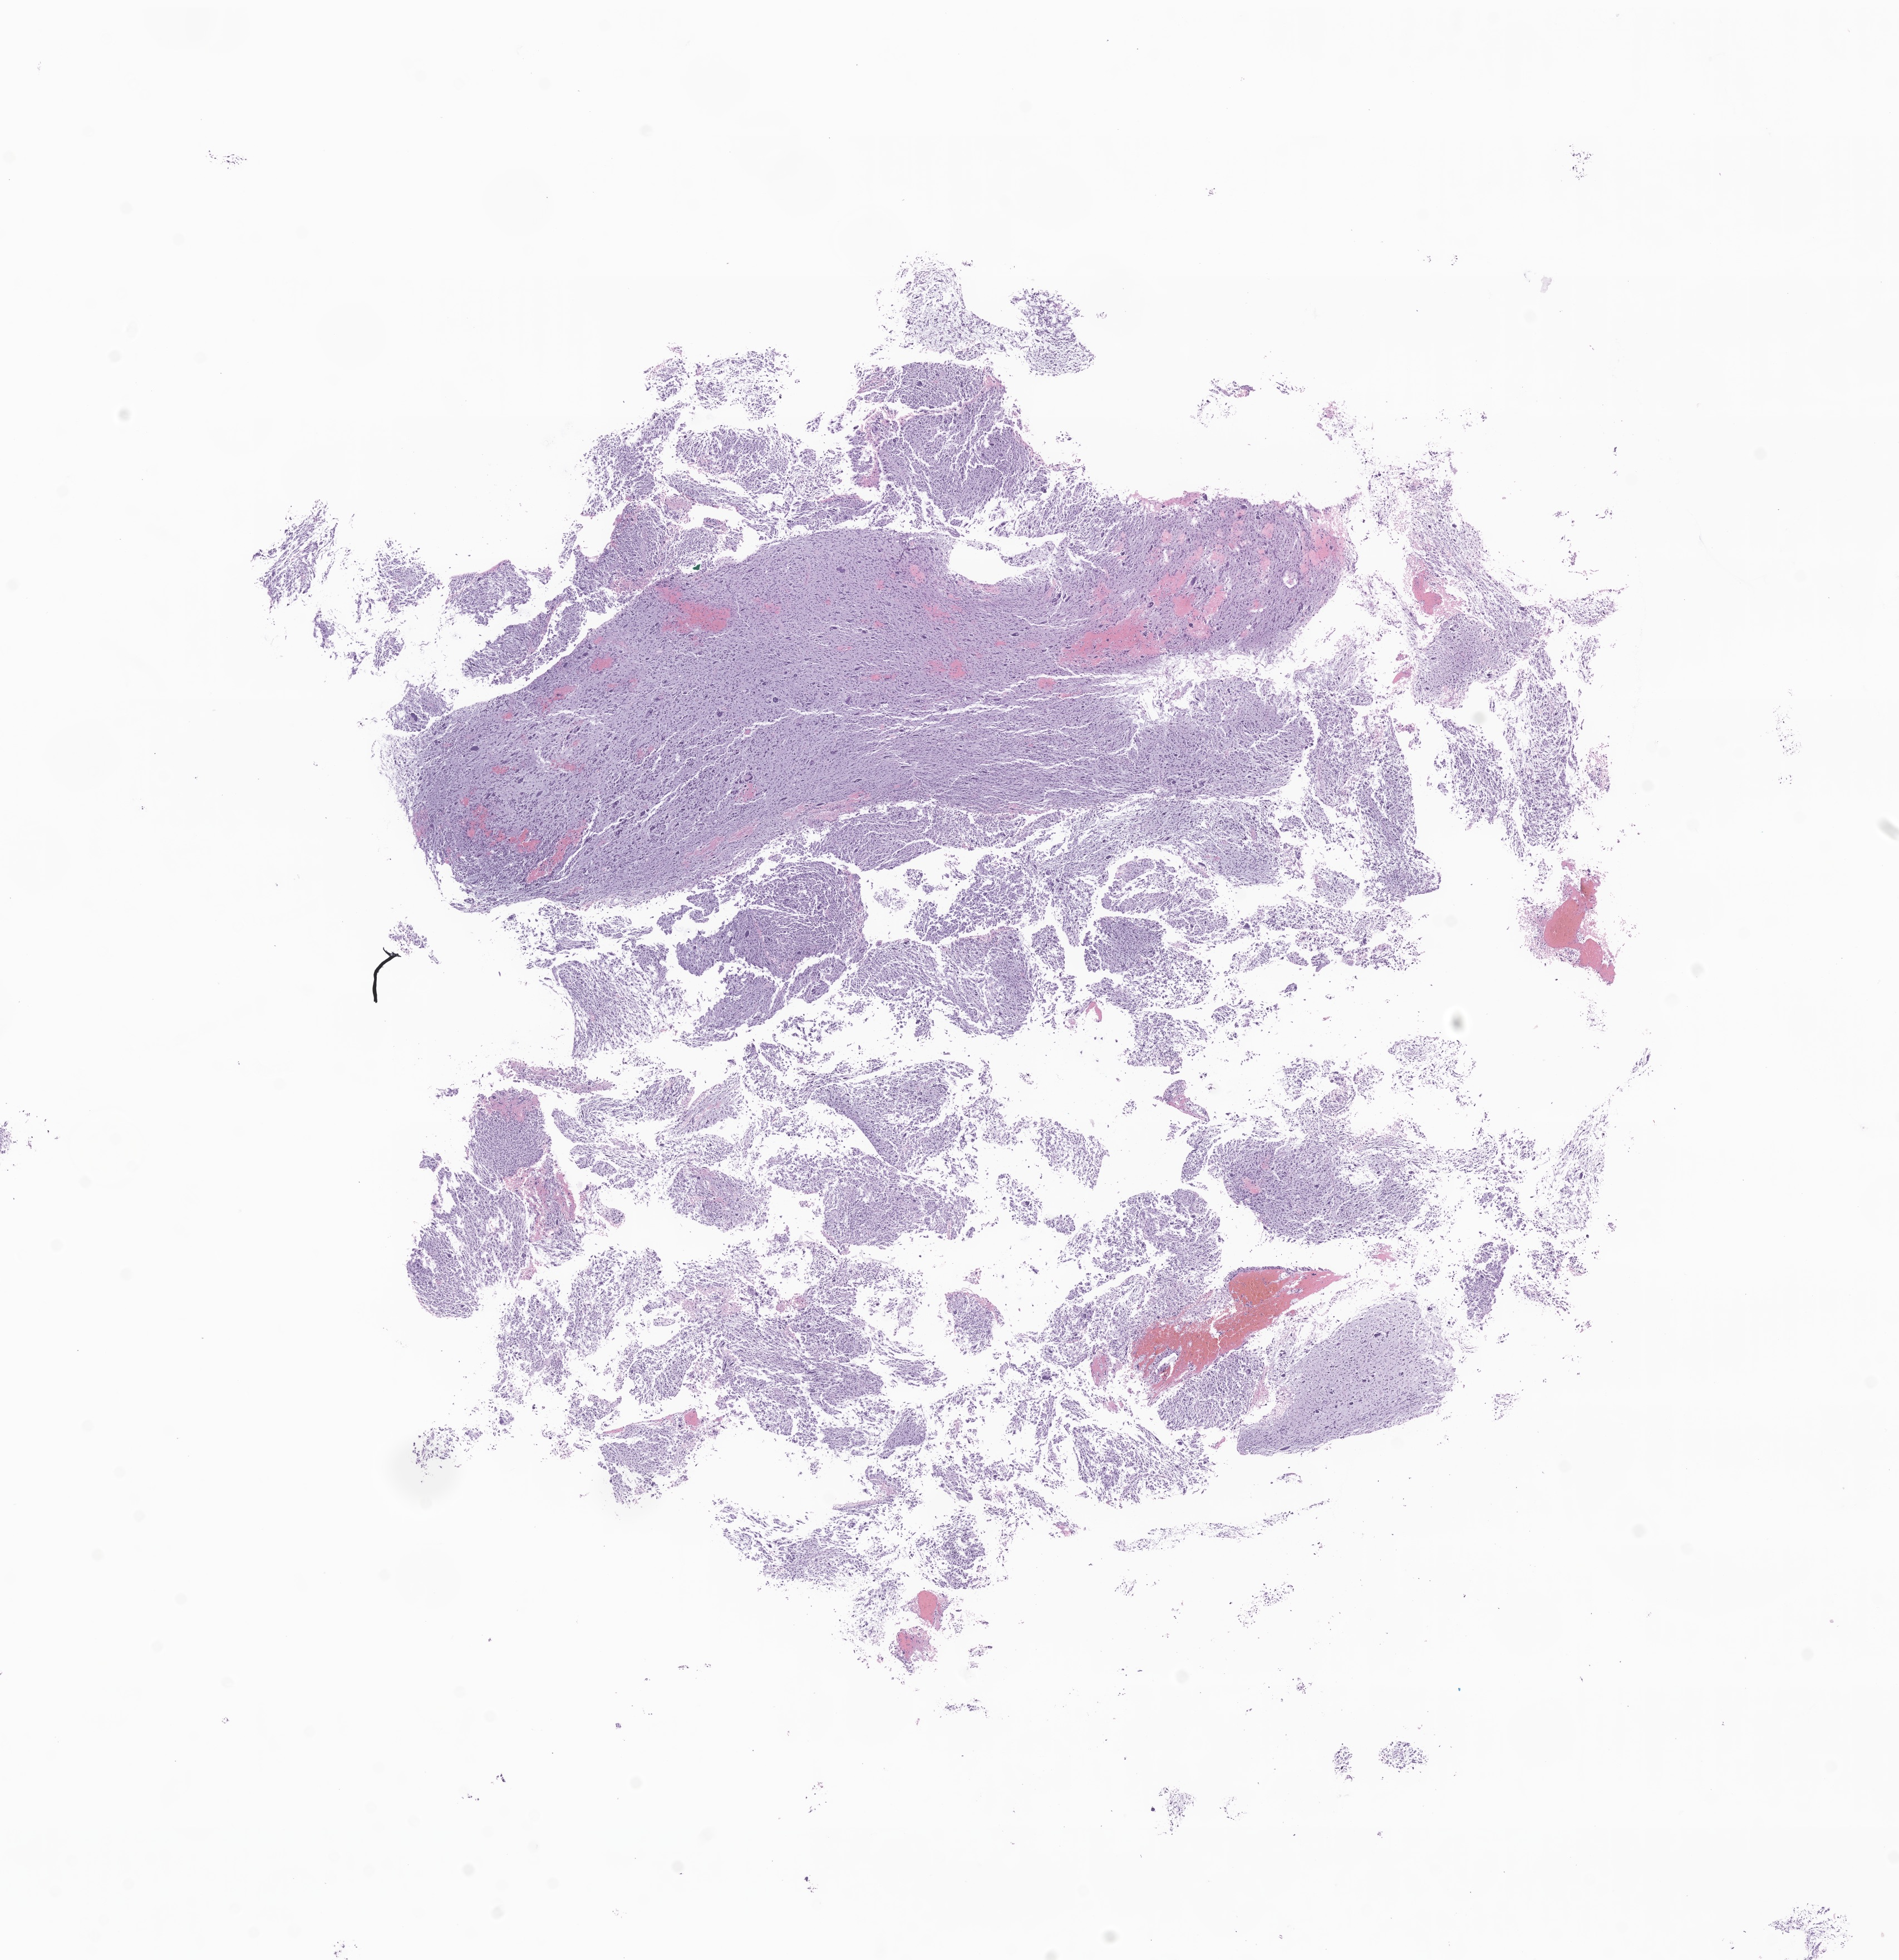
Haematoxylin and eosin whole-slide image of tumor tissue from the brain — shown as a low-resolution overview of the whole scanned area (about 14.4 x 14.8 mm); FFPE section. Patient: female, age 130 months (10 years 10 months).
Recorded diagnosis: Glioma, malignant.